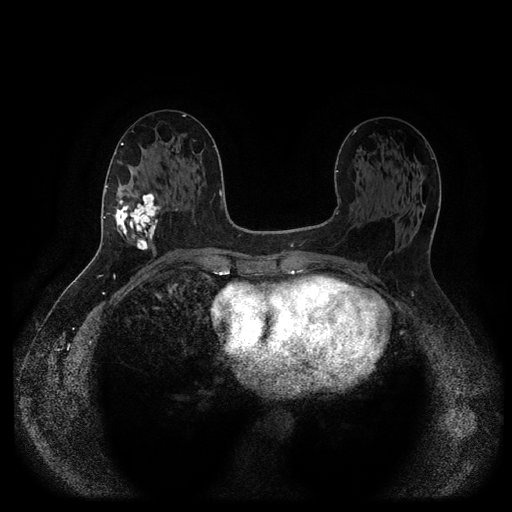
Breast MRI (dynamic contrast-enhanced, multi-phase), one axial slice. Slice 48 of 116 in the series (ordered by position). Dynamic contrast-enhanced series, time point 2 of 5 at this slice position (early post-contrast). 1.5 T. TE 2.6 ms, TR 5.3 ms. 2 mm slice thickness. 512 × 512 image matrix. Female patient, age 58 years.
Structures marked on this image (semi-automatically segmented with operator editing):
- breast lesion (labelled 'tumour' in the annotation; benign lesions carry a separate 'benign' label): box from (x=112, y=192) to (x=162, y=253) px